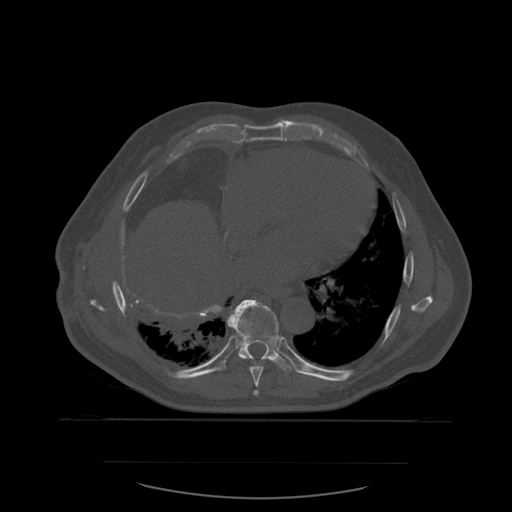
CT including the spine, one axial slice. Slice 350 of 590 in the series (ordered by position). Bone window (W 1800 / L 400 HU). 1.25 mm slice thickness. 512 × 512 image matrix, field of view 479 × 479 mm. Patient age 71 years. Case-level facts recorded for this patient, not image findings: primary cancer: lung; vertebrae with lytic lesions (as recorded): T1, T2, L5, S1.
Outlined on this slice (semi-automatic segmentation, software-assisted and operator-edited):
- T8 vertebra: box from (x=228, y=317) to (x=264, y=396) px
- T9 vertebra: (x=223, y=300)–(x=294, y=372)